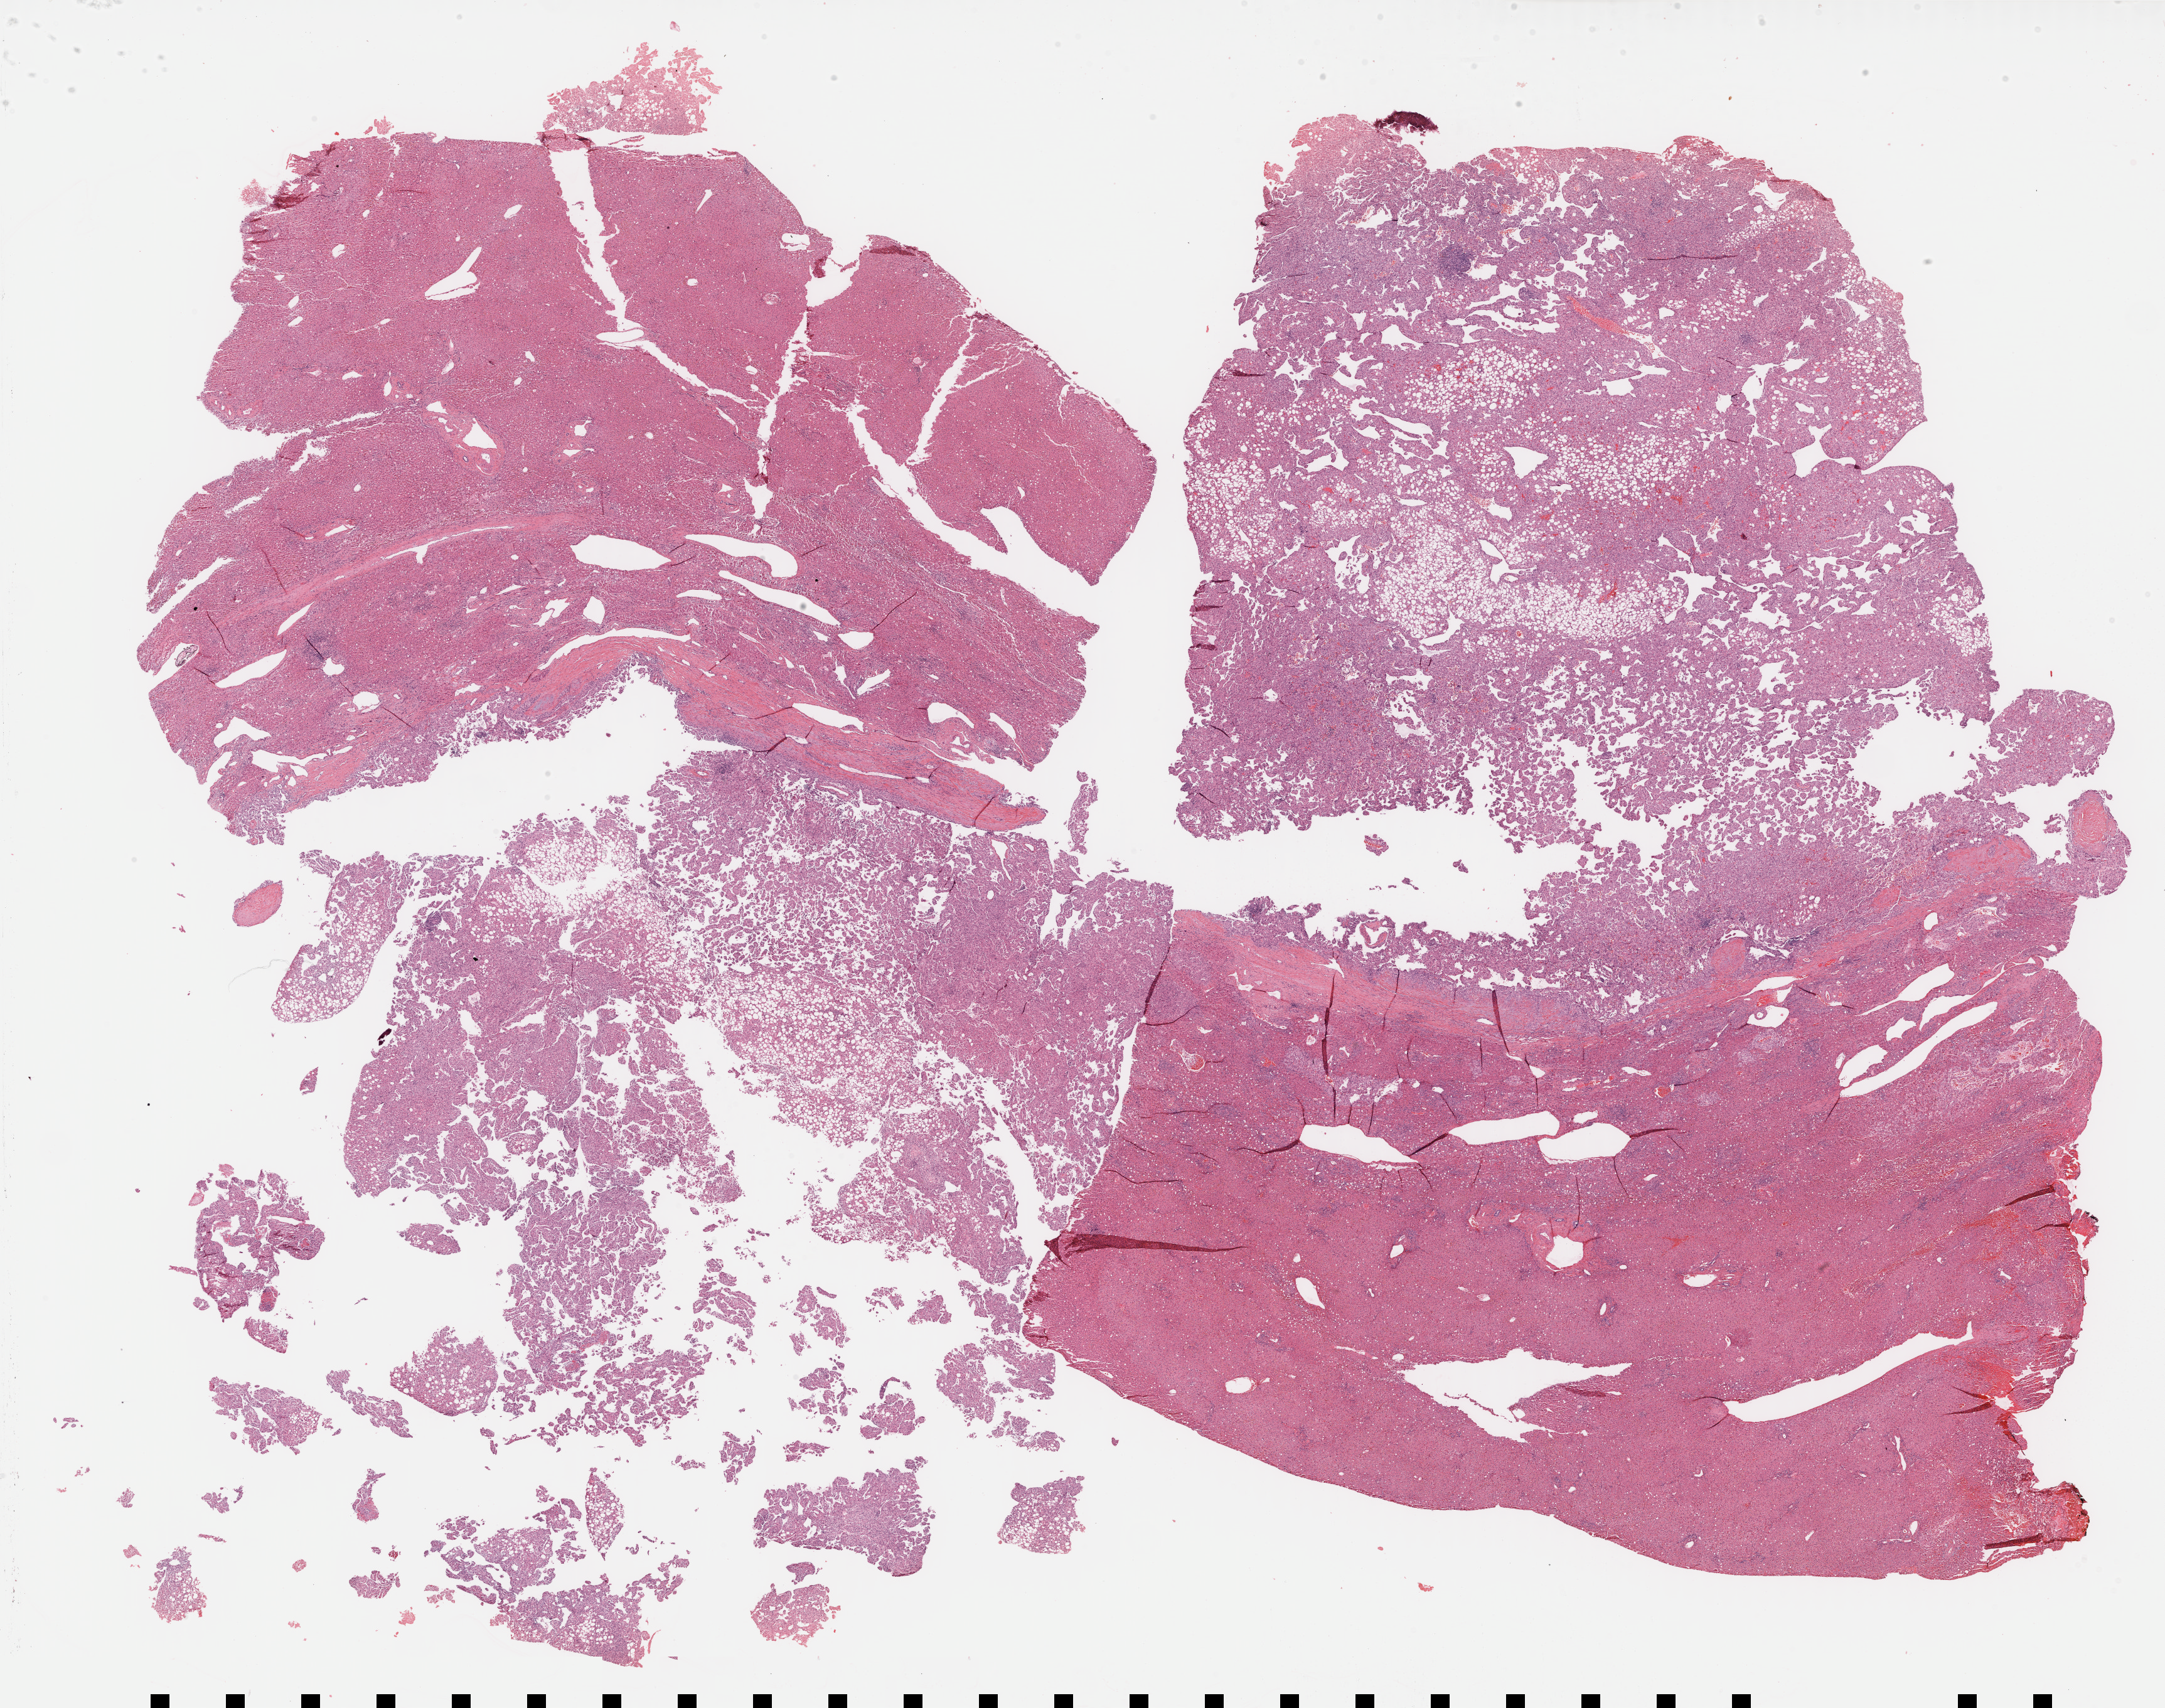
Digitized H&E-stained tissue section (whole slide) — a low-resolution overview of the entire scanned area, about 27.9 x 22.0 mm (slide scanned at 40x), formalin-fixed paraffin-embedded (FFPE) diagnostic section, sample: primary tumour, liver. Female, age 72 years at initial diagnosis. Histologic grade: G2 (moderately differentiated).
* histologic diagnosis: Hepatocellular carcinoma, NOS
* AJCC pathologic stage: II